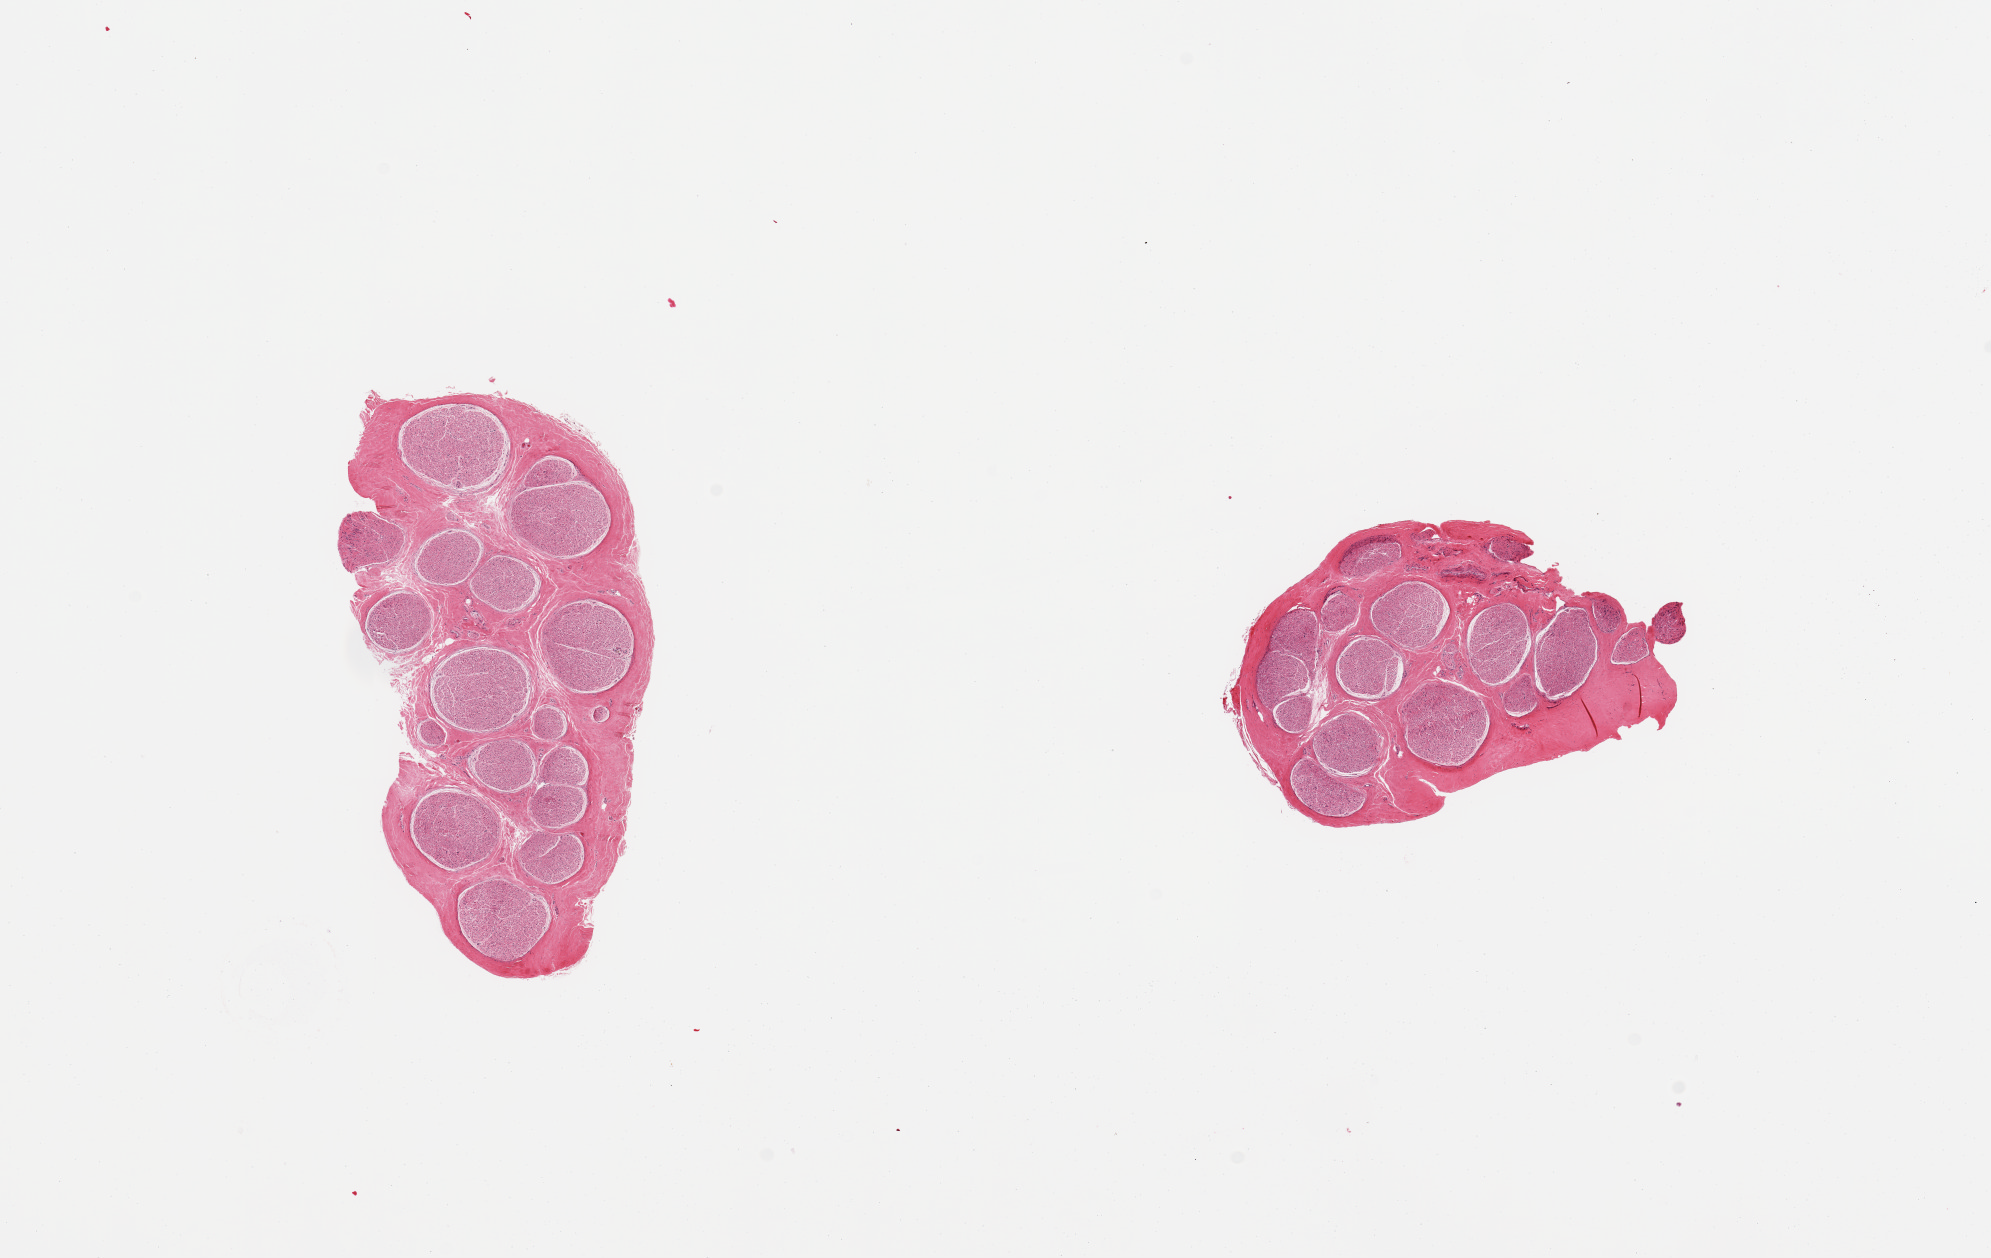
Haematoxylin and eosin whole-slide image, brightfield, a low-resolution overview of the entire scanned area, about 15.8 x 10.0 mm (slide scanned at 20x). PAXgene-fixed paraffin-embedded (PFPE) section. Section of tibial nerve (target tissue). Donor tissue sample. Donor sex: male.
• pathologist's review note for this sample: 2 pieces, no fat, excellent clean specimens